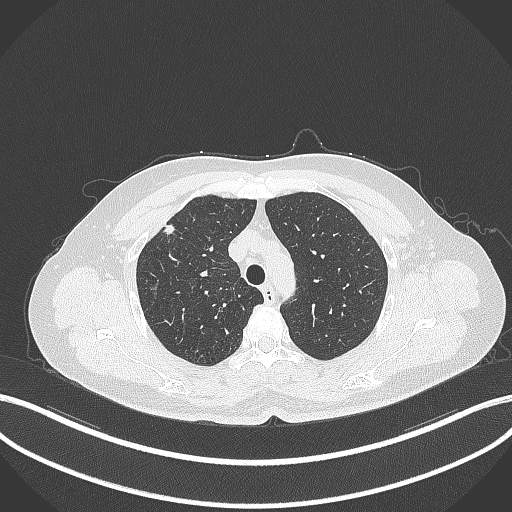
Chest CT, one axial slice. Slice 285 of 353 in the series (ordered by position). Reconstruction kernel B70f. 120 kVp. Lung window (W 1500 / L -600 HU). 1 mm slice thickness. 512 × 512 image matrix. Patient: female, 56 years. From the clinical record (not read from this slice): clinical TNM (as recorded): T1c N0 M0.
Outlined on this slice (rectangle marked by the reading radiologist):
- lung tumour (recorded histology: adenocarcinoma): box from (x=164, y=222) to (x=180, y=240) px